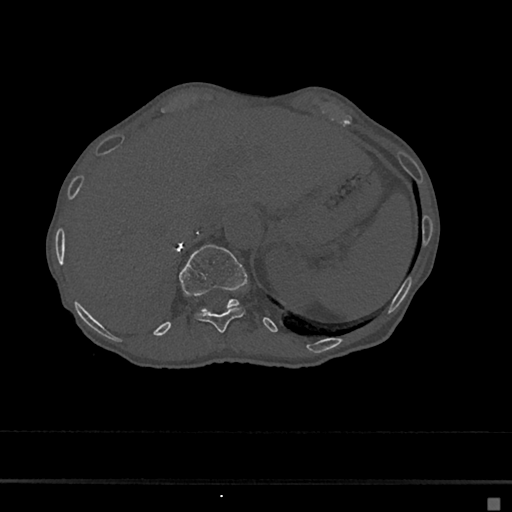
CT including the spine, one axial slice. Reconstruction kernel Br40s/3. 120 kVp. Bone window (W 1800 / L 400 HU). 512 × 512 image matrix, field of view 360 × 360 mm. Patient: female, 68 years. Case-level facts recorded for this patient, not image findings: primary cancer: renal.
Annotated regions visible in this slice (semi-automatically segmented with operator editing):
- T11 vertebra: bounding box (x1, y1, x2, y2) in pixels: (196, 308, 244, 333)
- T12 vertebra: (178, 244, 247, 311)